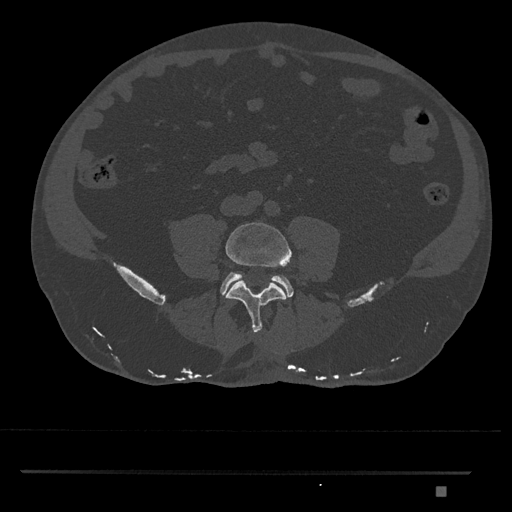
CT including the spine, one axial slice. Reconstruction kernel Br40s/3. Bone window (W 1800 / L 400 HU). 512 × 512 image matrix. Patient: male, 65 years. From the clinical record (not read from this slice): primary cancer: prostate.
Annotated regions visible in this slice (semi-automatic segmentation, software-assisted and operator-edited):
- L4 vertebra: bounding box (x1, y1, x2, y2) in pixels: (225, 222, 292, 333)
- L5 vertebra: (220, 272, 294, 297)